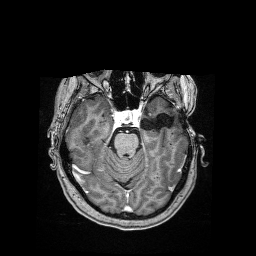
Brain MRI from a brain-tumour surgery series, one axial slice. Position 107 of 176 along the scan axis. T1-weighted post-contrast. 256 × 256 image matrix, field of view 256 × 256 mm. Case-level facts recorded for this patient, not image findings: histopathology: Dysembryoplastic neuroepithelial tumor; WHO grade: 1; IDH mutation: no; tumour location: Left Temporal.
Annotated regions visible in this slice (manually delineated by an expert):
- tumour: bounding box <148,113,153,117> (left, top, right, bottom; pixels)